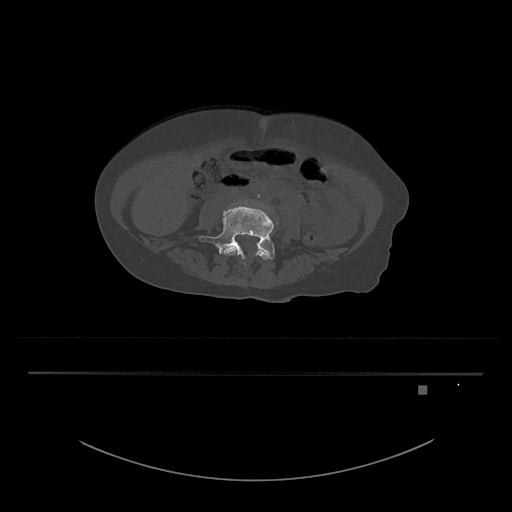
CT including the spine, one axial slice; position 324 of 797 along the scan axis; reconstruction kernel Br40s/3; 120 kVp; bone window (W 1800 / L 400 HU); 0.5 mm slice thickness; 512 × 512 image matrix. Female patient, age 57 years. From the clinical record (not read from this slice): primary cancer: cervical.
Outlined on this slice (semi-automatically segmented with operator editing):
- L4 vertebra: box from (x=223, y=241) to (x=271, y=265) px